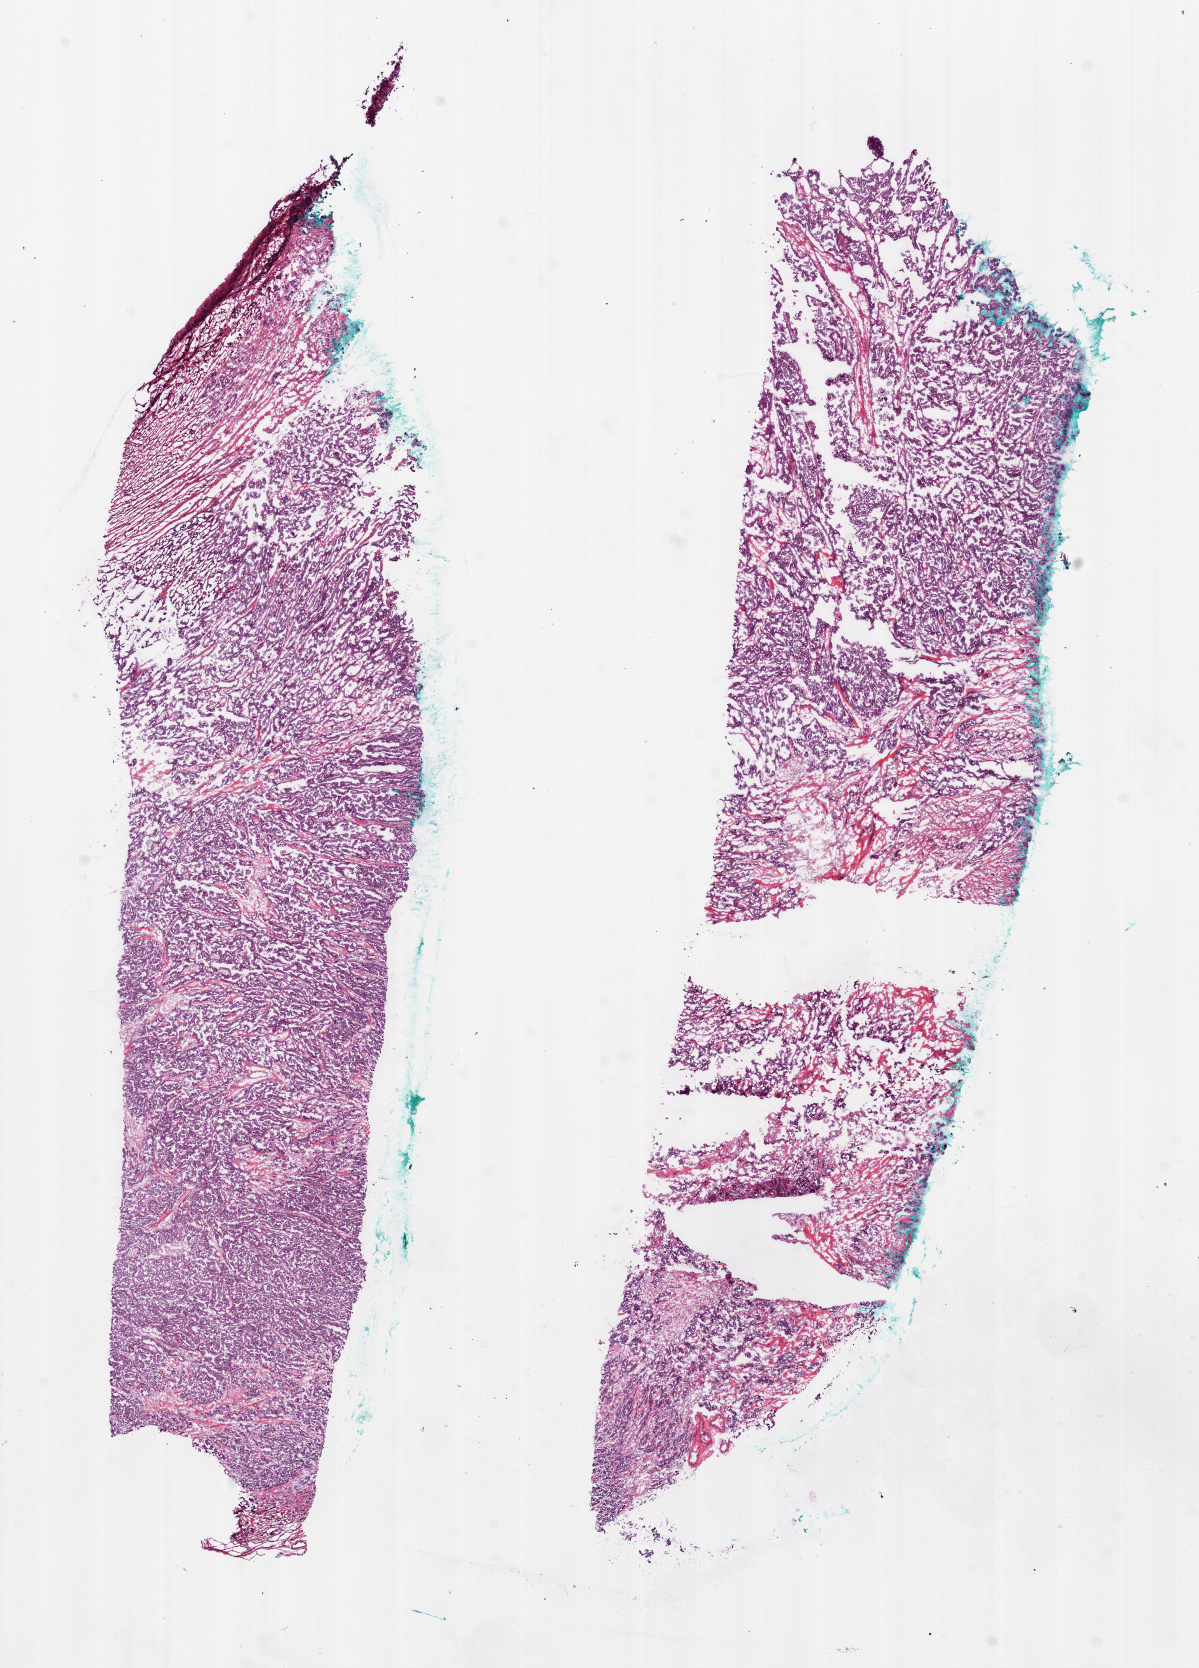
Whole-slide histology image, H&E-stained — low-resolution overview of the scanned area, about 9.7 x 13.5 mm (from a 20x scan); frozen section from the bottom of the tissue portion; primary tumour sample from the ovary. Female patient; age at initial diagnosis 71 years. Histologic grade: G3 (poorly differentiated). Pathologist review of this section (percent, as recorded): tumour cells 85%, tumour nuclei 95%, normal cells 15%, stromal cells 0%, necrosis 0%.
- FIGO stage: IIIC
- diagnosis: Serous cystadenocarcinoma, NOS